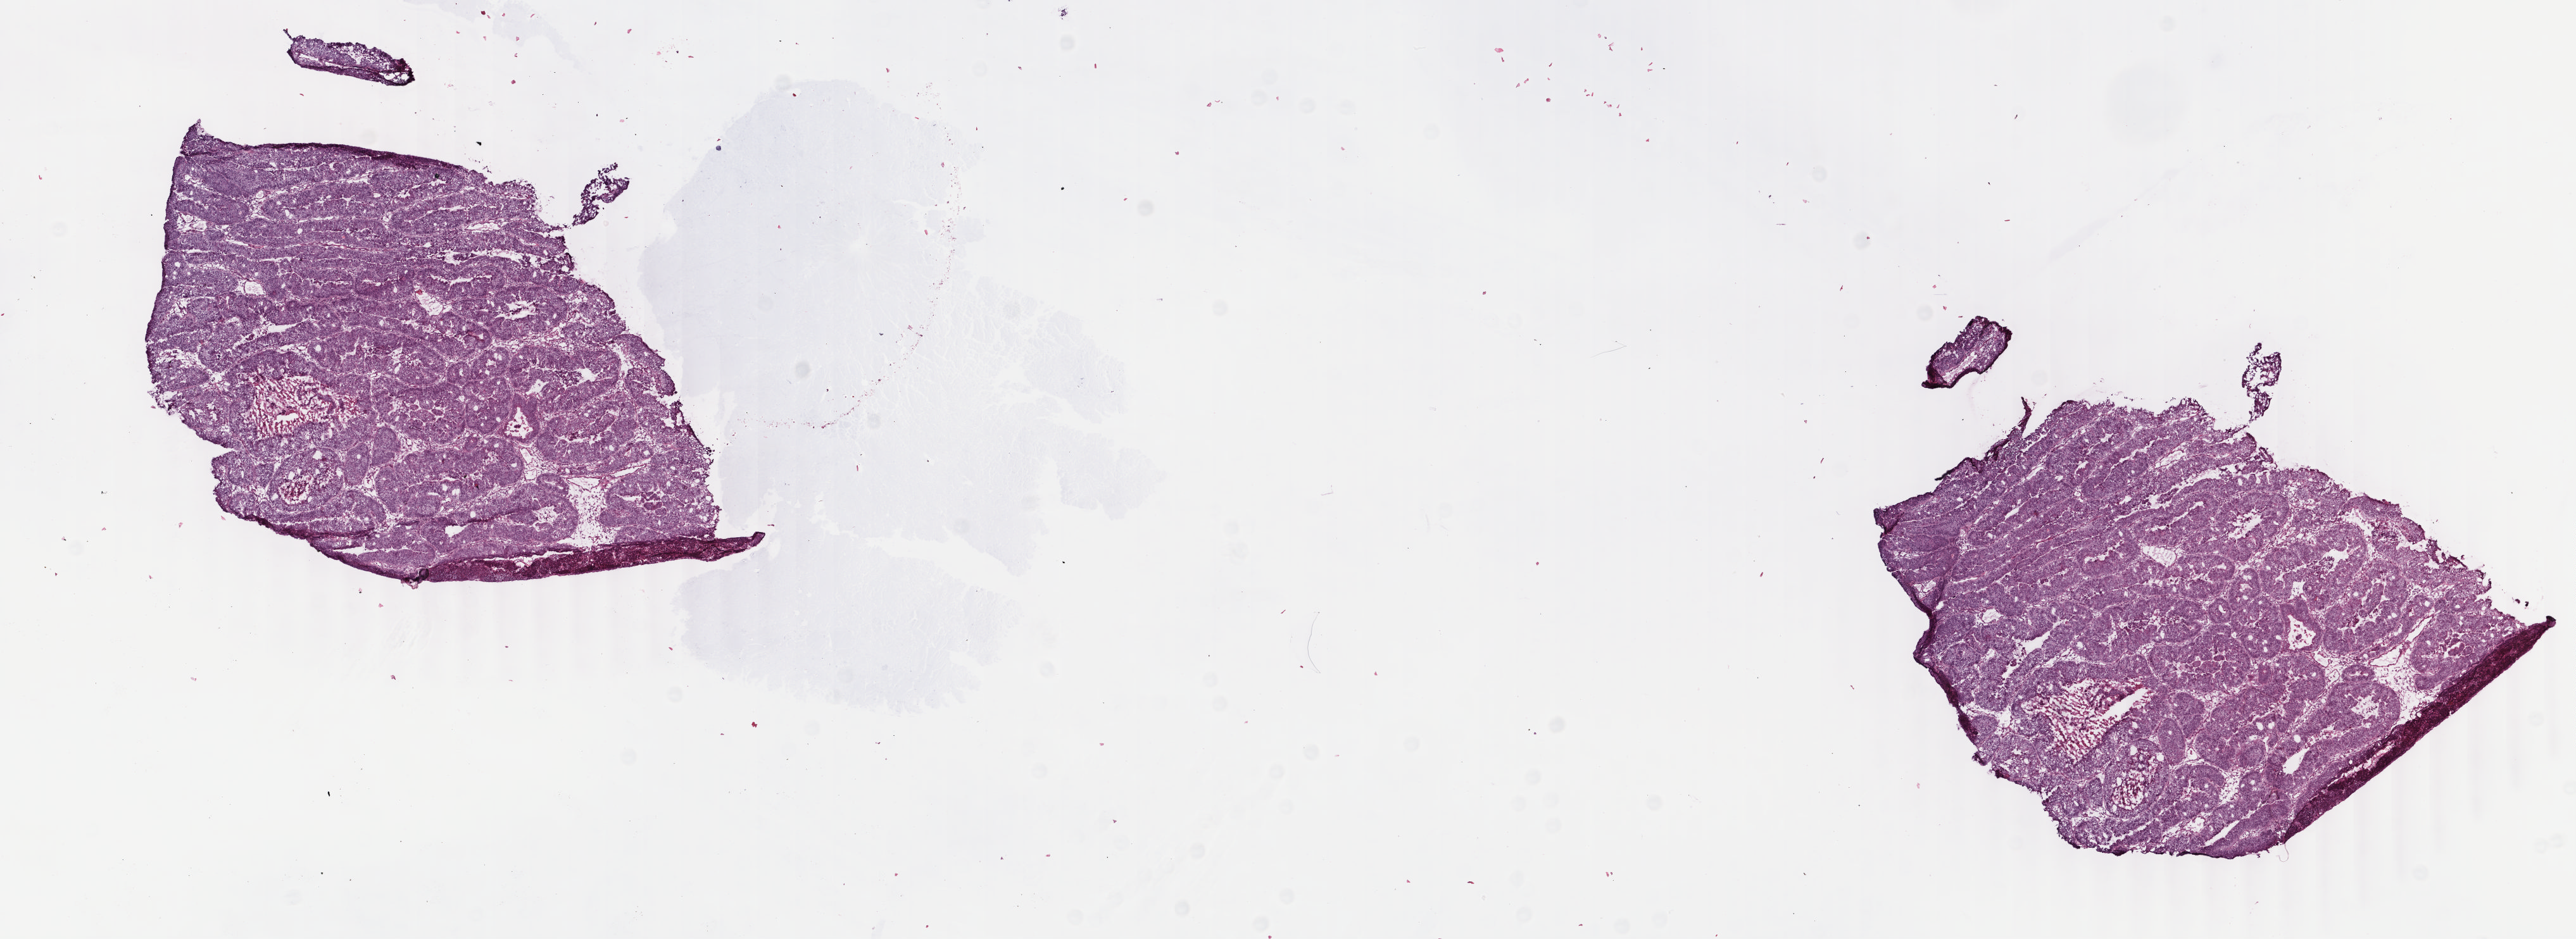
Digitized H&E tissue section (whole slide) — whole scanned area (about 16.2 x 5.9 mm, from a 40x scan) shown as a low-resolution overview, frozen section from the top of the tissue portion, sample: primary tumour, rectum. Male, age 55 years at initial diagnosis. Pathologist review of this section (percent, as recorded): tumour cells 98%, tumour nuclei 95%, normal cells 0%, stromal cells 1%, necrosis 1%. Inflammatory infiltration, as recorded: lymphocyte infiltration 2%, monocyte infiltration 1%, neutrophil infiltration 0%.
• pathologic diagnosis: Adenocarcinoma, NOS
• lymph nodes positive (case pathology): 4 of 19 examined
• AJCC pathologic stage: IV (6th edition)
• TNM: T3 N2 M1